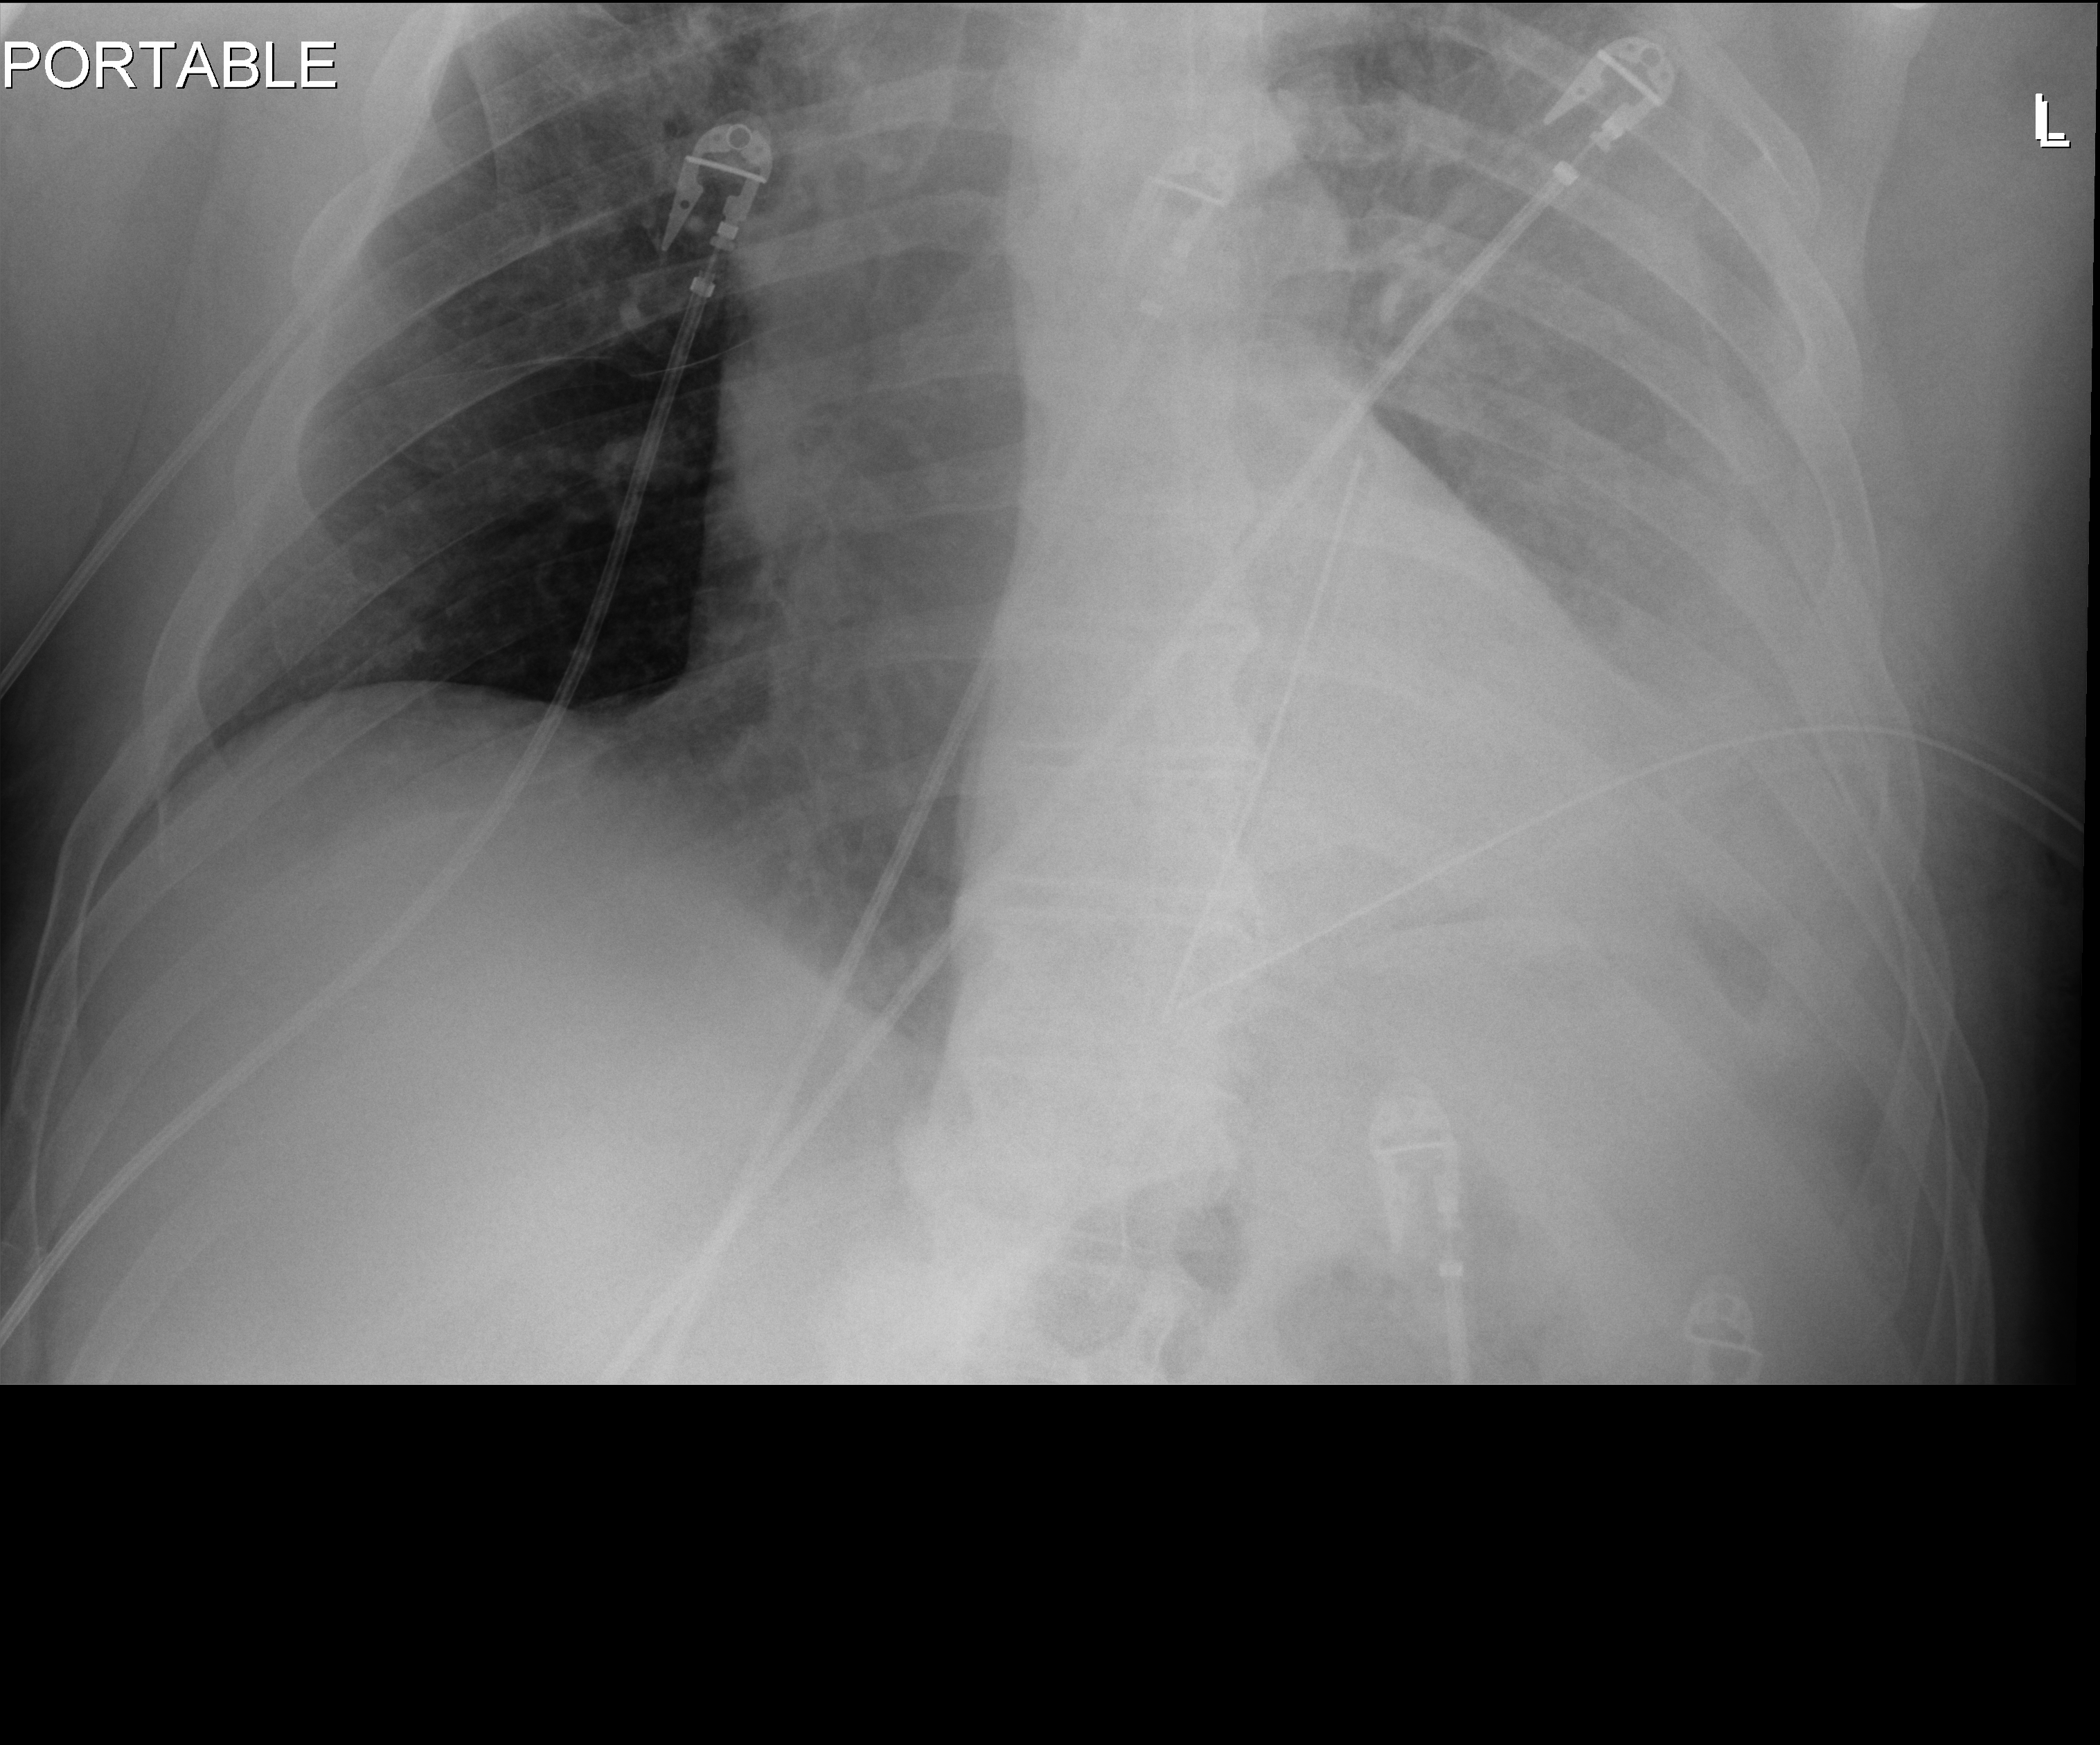
Chest X-ray (portable). Male patient hospitalised with COVID-19, age 18–59 years.
Hospital-stay facts (about this admission, not read from this image; timing relative to this image not recorded): admitted to intensive care during this hospital stay: no; mechanically ventilated during this hospital stay: no.